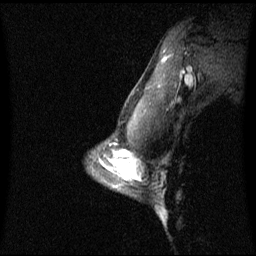
Breast MRI (dynamic contrast-enhanced), one sagittal slice; position 50 of 60 along the scan axis; dynamic contrast-enhanced series, image 2 of 3 at this slice position (ordered by acquisition); 1.5 T; TE 4.2 ms, TR 8.4 ms; 2.3 mm slice thickness; 256 × 256 image matrix, field of view 240 × 240 mm. Female patient, age 42 years. Case-level facts recorded for this patient, not image findings: setting: breast cancer imaged before/during neoadjuvant chemotherapy; receptor status: triple-negative.
Structures marked on this image (semi-automatically segmented with operator editing):
- analysis volume of interest (the breast-tissue region the enhancement analysis was run in; not a lesion): bounding box [x1, y1, x2, y2] px = [106, 156, 137, 189]
- tumour enhancement mask (voxels above the 70 % enhancement threshold inside the analysis volume of interest): [122, 156, 136, 179]